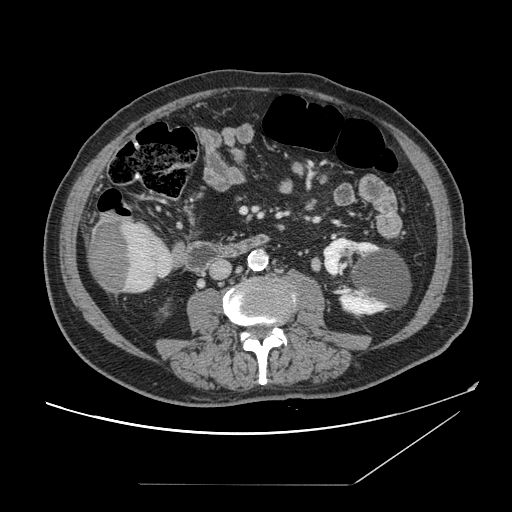
Contrast-enhanced abdominal CT, one axial slice; 120 kVp; intravenous contrast given; soft-tissue window (W 400 / L 40 HU); 2.5 mm slice thickness; 512 × 512 image matrix, field of view 416 × 416 mm. Male patient, age 80 years. From the clinical record (not read from this slice): diagnosis: colorectal cancer liver metastases, imaged before liver resection; multiple liver metastases: no; largest metastasis: 2.2 cm; disease in both lobes: no.
Structures marked on this image (expert manual segmentation):
- liver: box from (x=88, y=215) to (x=174, y=294) px
- liver metastasis: (x=92, y=220)–(x=133, y=291)